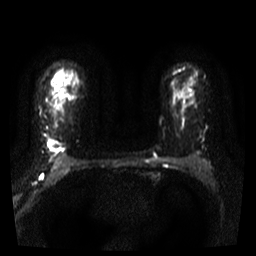
Breast MRI, one axial slice. Slice 27 of 36 in the series (ordered by position). Diffusion-weighted series; image 2 of 4 stored at this slice position (different b-values; order by instance number). 3 T. 5 mm slice thickness. 256 × 256 image matrix, field of view 300 × 300 mm. Female patient.
Outlined on this slice (manually delineated by an expert):
- tumour on diffusion-weighted imaging: bounding box (x1, y1, x2, y2) in pixels: (49, 140, 58, 152)